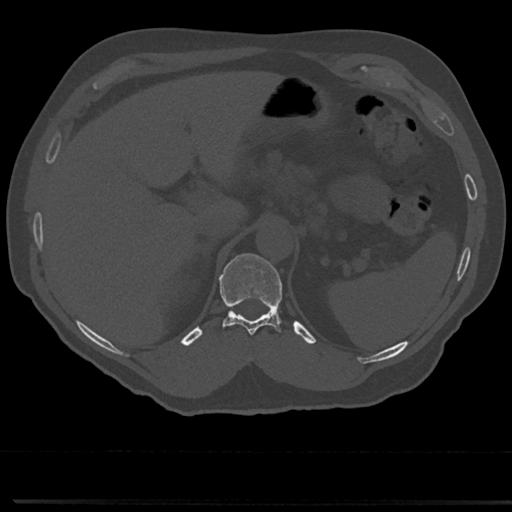
CT including the spine, one axial slice. Position 201 of 817 along the scan axis. Reconstruction kernel Br40s/3. Bone window (W 1800 / L 400 HU). 0.5 mm slice thickness. 512 × 512 image matrix. Male patient, age 61 years. Case-level facts recorded for this patient, not image findings: primary cancer: prostate.
Annotated regions visible in this slice (semi-automatic segmentation, software-assisted and operator-edited):
- T11 vertebra: bounding box [x1, y1, x2, y2] px = [219, 253, 283, 336]